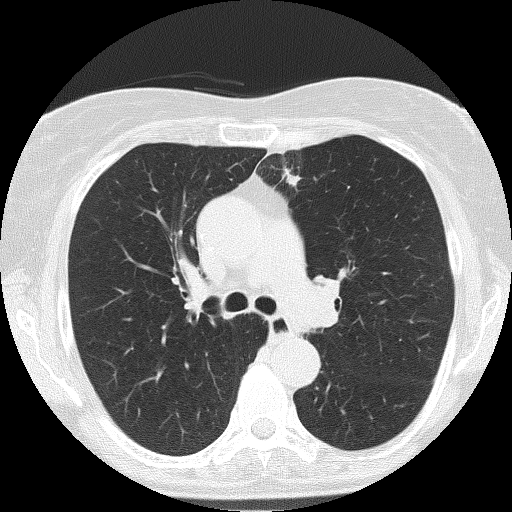
Low-dose screening chest CT, one axial slice; position 112 of 166 along the scan axis; lung window (W 1500 / L -600 HU); 2 mm slice thickness; 512 × 512 image matrix, field of view 303 × 303 mm.
Annotated regions visible in this slice (expert manual segmentation):
- lesion 2 (nodule, upper lobe of left lung): bounding box <284,170,297,184> (left, top, right, bottom; pixels)